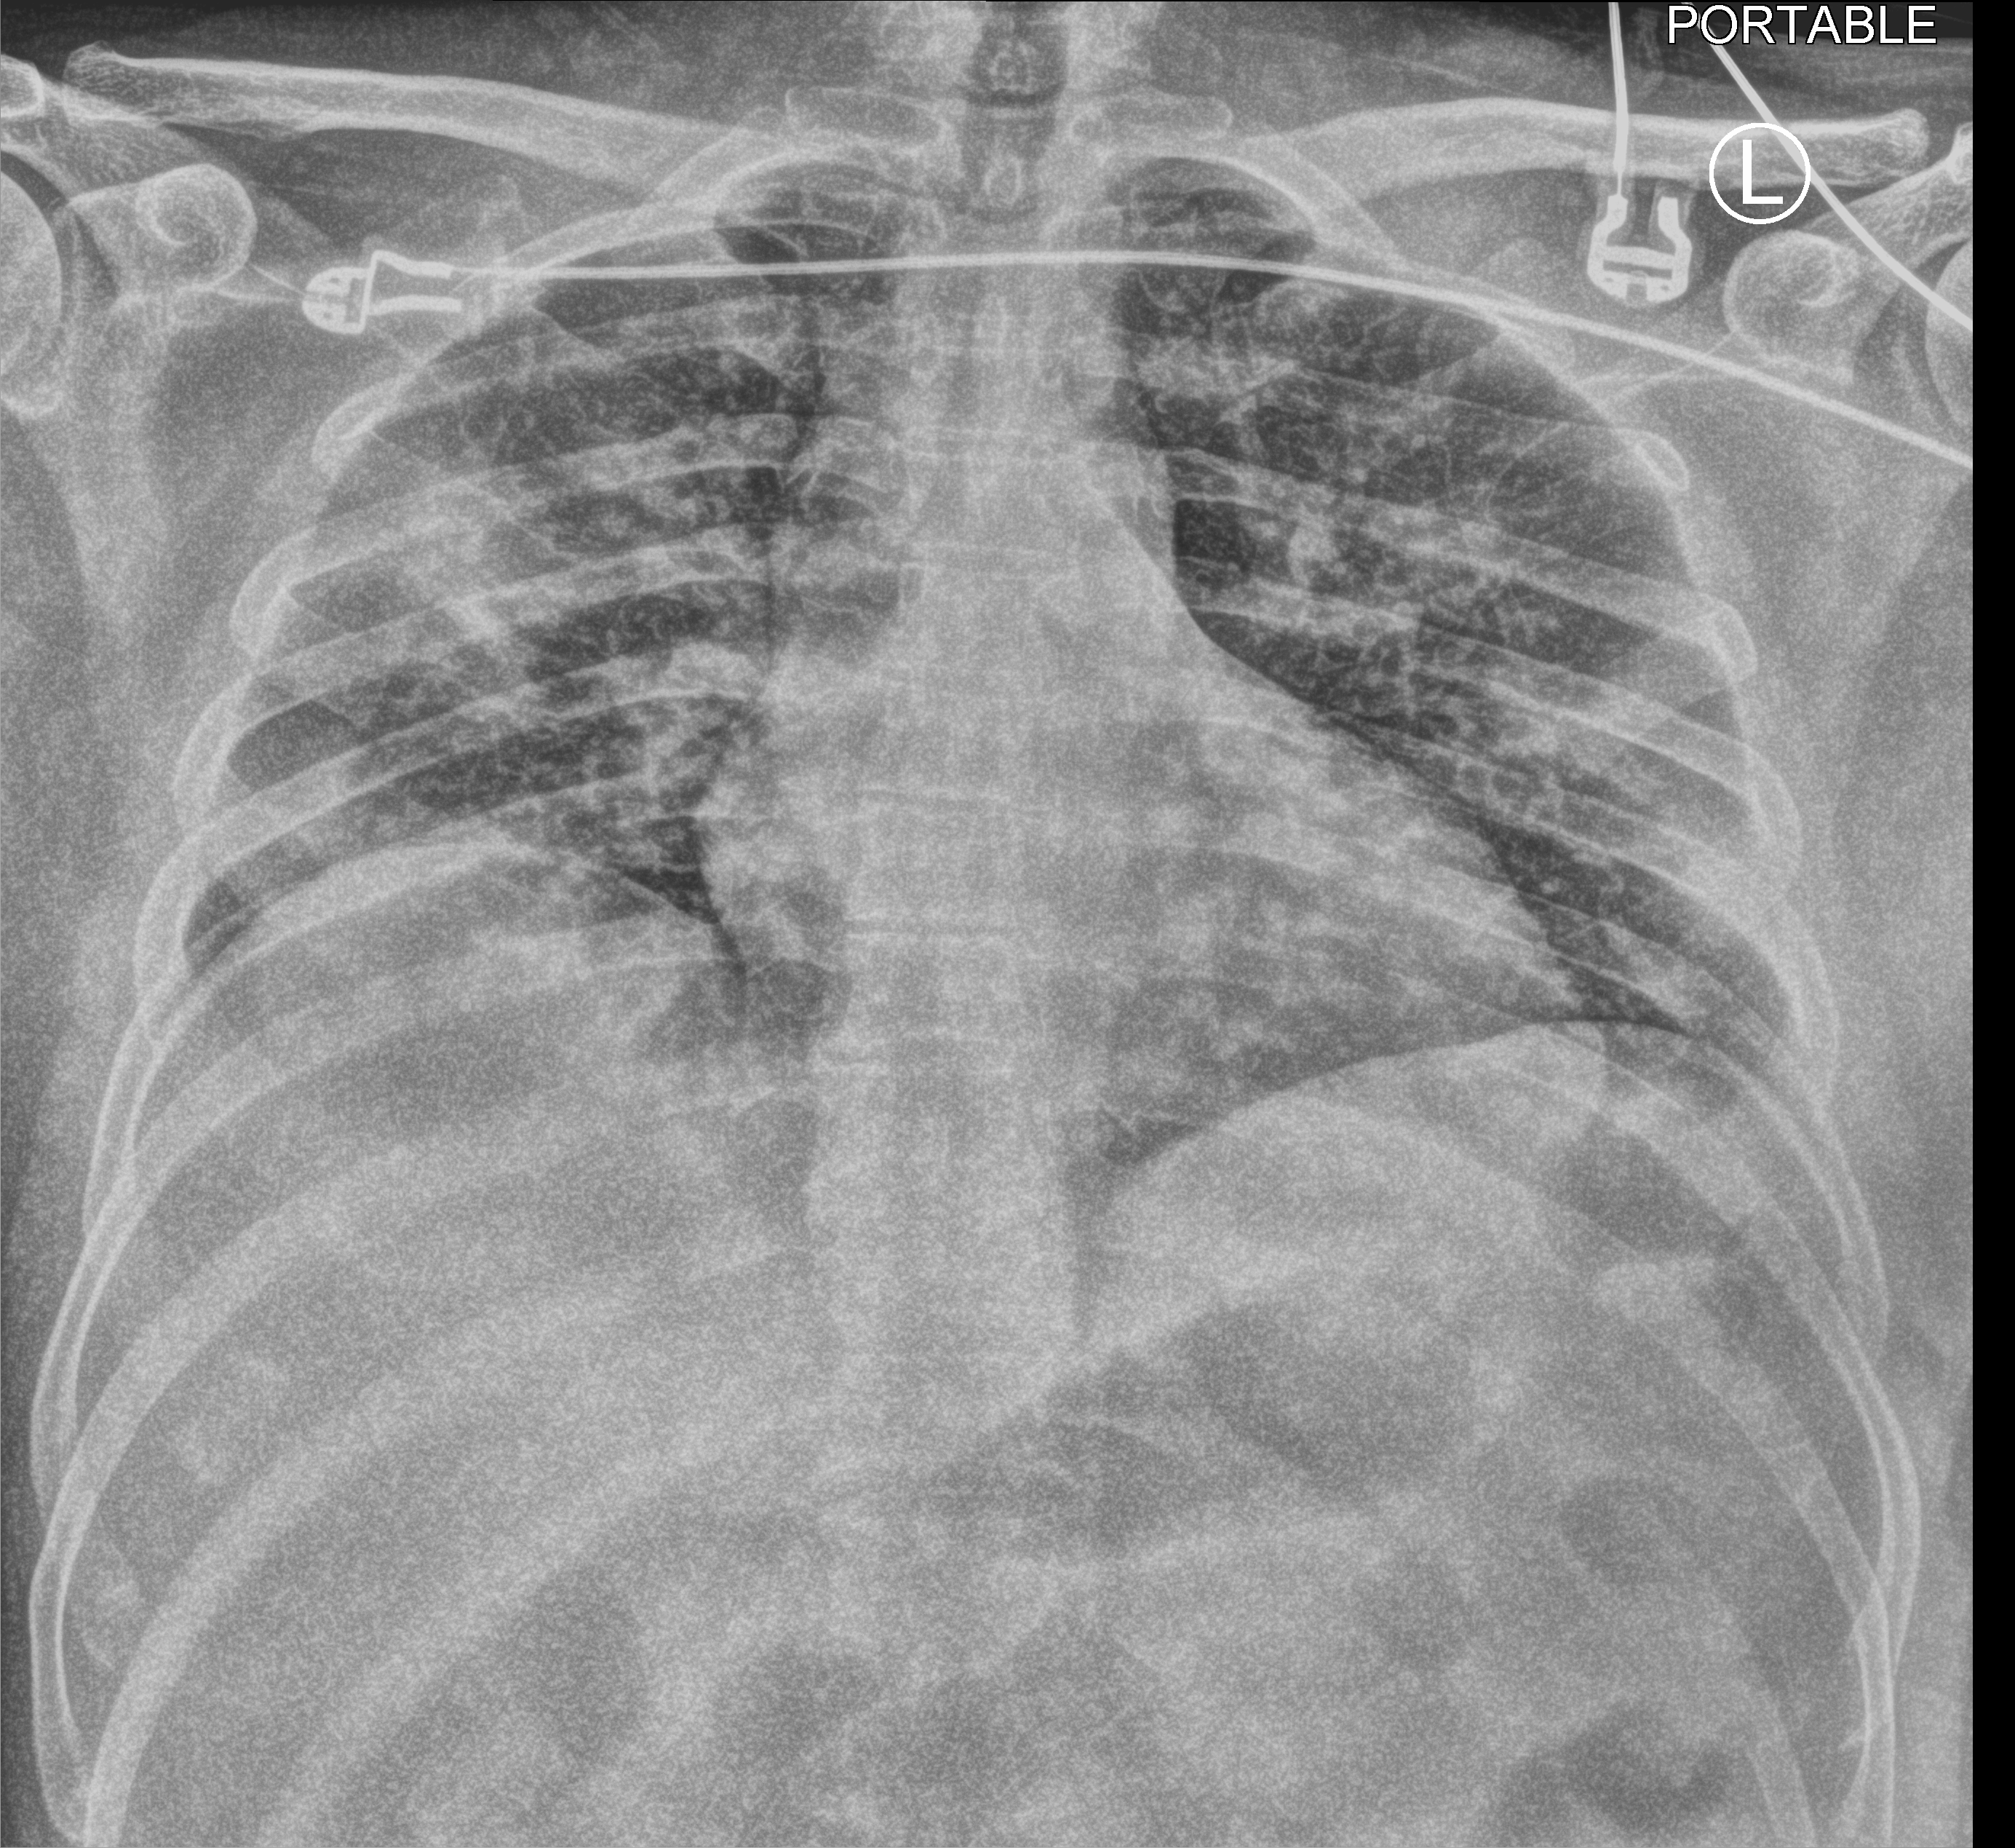
Bedside chest radiograph (computed radiography). Male patient hospitalised with COVID-19, age 18–59 years.
From the hospital-stay record, not from the radiograph (when in the stay this image was taken is not recorded):
- admitted to intensive care during this hospital stay: no
- other chronic lung disease (admission record): no
- mechanically ventilated during this hospital stay: no